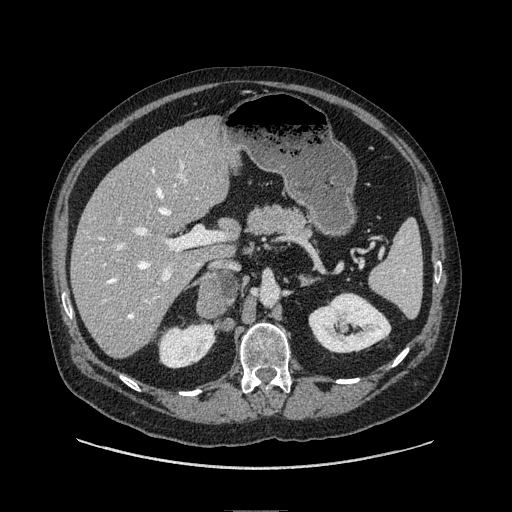
Contrast-enhanced abdominal CT, one axial slice. Slice 48 of 149 in the series (ordered by position). Soft-tissue window (W 400 / L 40 HU). 1.25 mm slice thickness. 512 × 512 image matrix. Male patient. From the clinical record (not read from this slice): diagnosis: adrenocortical carcinoma; tumour side: right adrenal; tumour size at pathology: 7.5 cm; Ki-67 index: 15 %; stage (as recorded): 2.
Annotated regions visible in this slice (semi-automatically segmented with operator editing):
- mass: bounding box <198,272,240,315> (left, top, right, bottom; pixels)